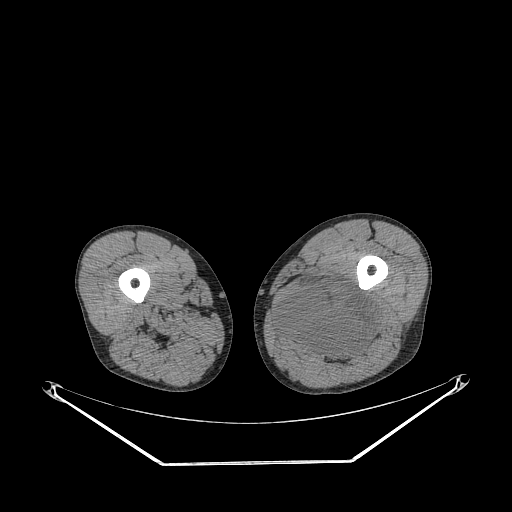
CT of an extremity soft-tissue mass (from a PET/CT study), one axial slice; position 239 of 267 along the scan axis; soft-tissue window (W 400 / L 40 HU); 3.75 mm slice thickness; 512 × 512 image matrix. Male patient. Case-level facts recorded for this patient, not image findings: histological type: undifferentiated pleomorphic liposarcoma; grade: high; site of the primary tumour: left thigh.
Outlined on this slice (expert contour drawn on MRI and transferred to this co-registered scan by the dataset authors):
- gross tumour volume including surrounding oedema: box from (x=278, y=283) to (x=378, y=362) px
- gross tumour volume (mass): (x=278, y=283)–(x=378, y=359)